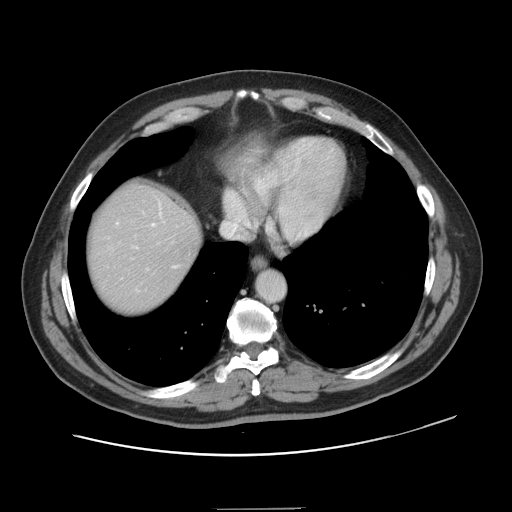
Contrast-enhanced abdominal CT, one axial slice. Position 132 of 143 along the scan axis. Soft-tissue window (W 400 / L 40 HU). 2.5 mm slice thickness. 512 × 512 image matrix, field of view 402 × 402 mm. Male patient, age 62 years. Case-level facts recorded for this patient, not image findings: diagnosis: colorectal cancer liver metastases, imaged before liver resection; multiple liver metastases: yes; largest metastasis: 2.7 cm; disease in both lobes: no.
Outlined on this slice (manually delineated by an expert):
- hepatic veins: bounding box <117,213,161,249> (left, top, right, bottom; pixels)
- liver: <88,186,200,314>
- planned liver remnant (the part of the liver to remain after resection): <88,186,200,302>
- portal vein (with intrahepatic branches): <159,206,161,211>